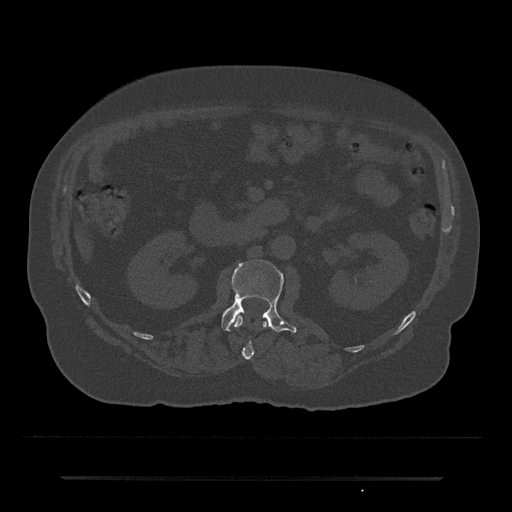
CT including the spine, one axial slice. Slice 27 of 797 in the series (ordered by position). Reconstruction kernel Br40s/3. 120 kVp. Bone window (W 1800 / L 400 HU). 512 × 512 image matrix, field of view 437 × 437 mm. Male patient, age 69 years. From the clinical record (not read from this slice): primary cancer: prostate.
Structures marked on this image (semi-automatic segmentation, software-assisted and operator-edited):
- L1 vertebra: box from (x=234, y=315) to (x=267, y=360) px
- L2 vertebra: (x=221, y=260)–(x=297, y=333)